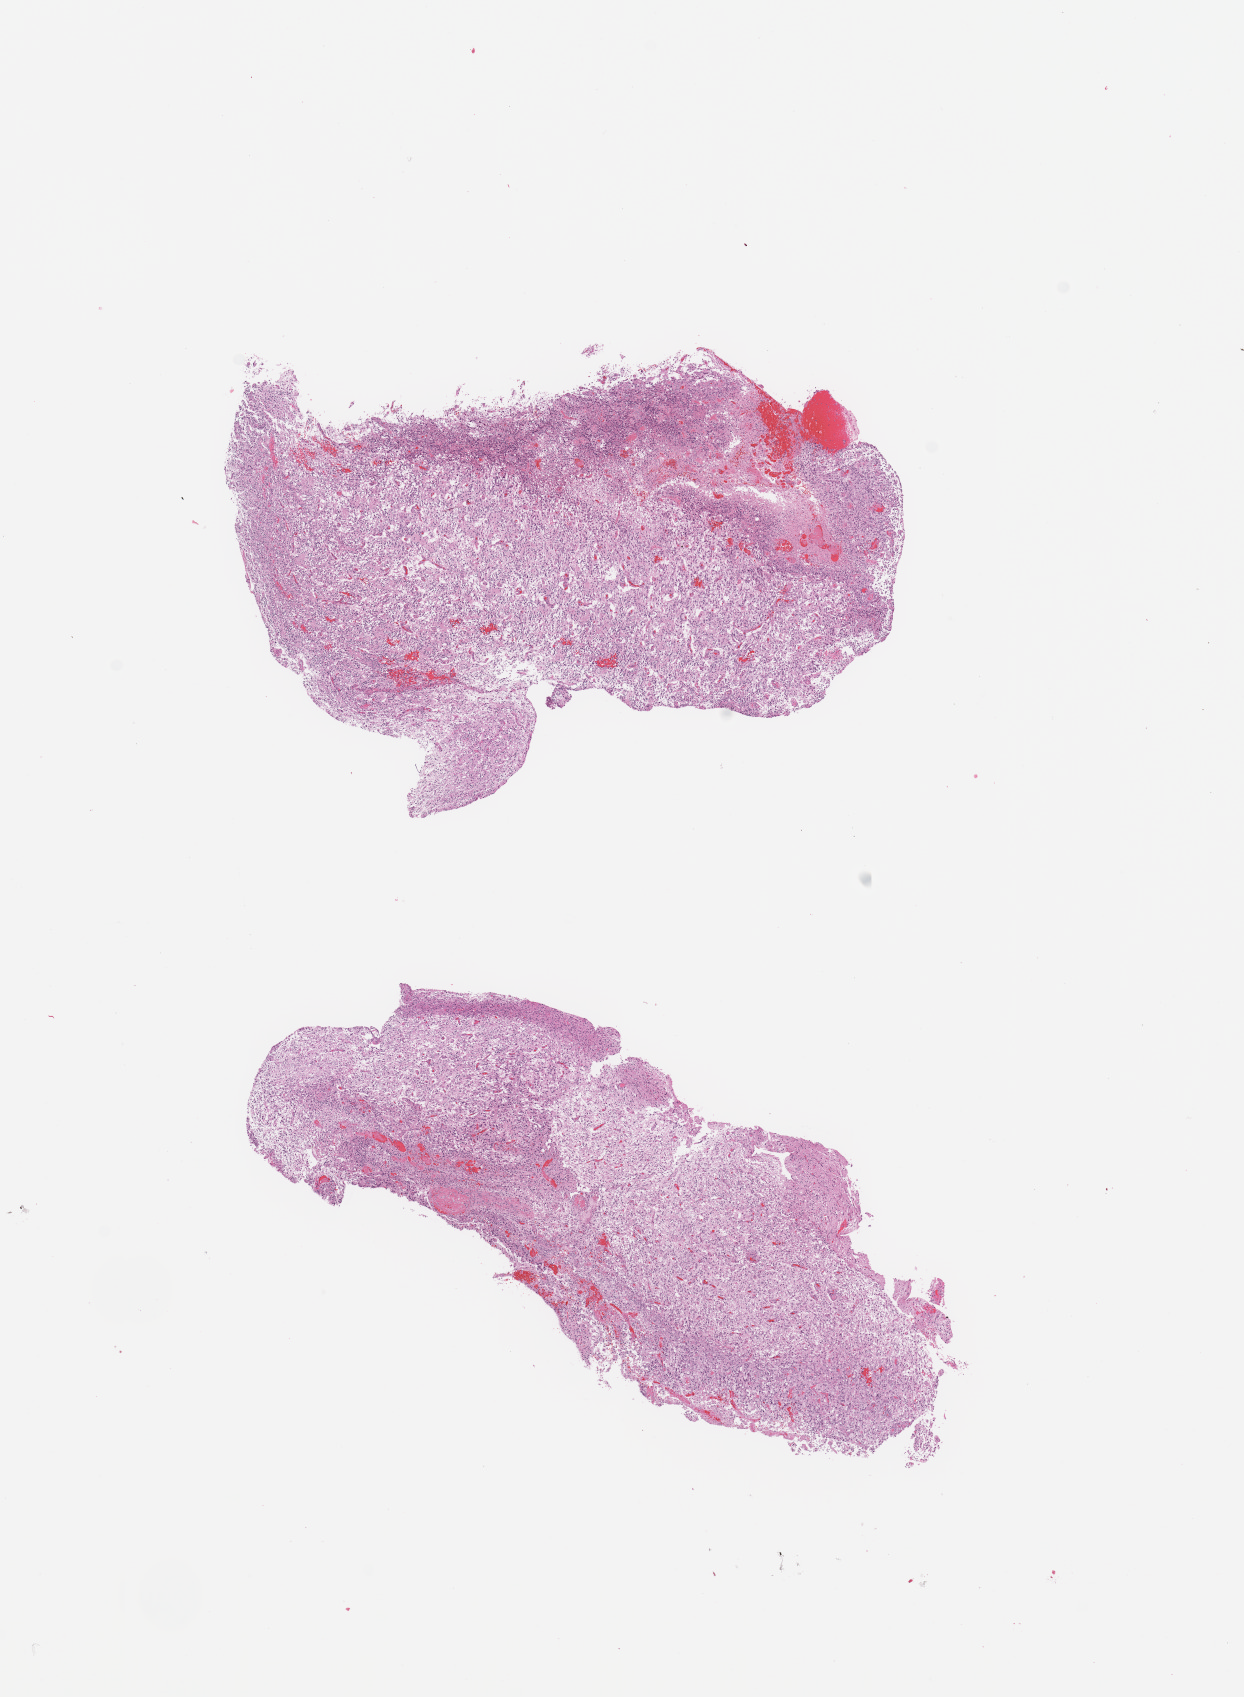
Whole-slide histology image, H&E-stained, a low-resolution overview of the entire scanned area, about 9.8 x 13.4 mm (acquisition: 20x scan), tumour tissue sample, sampled site: brain. 59-year-old male patient. Pathologist review of this section (percent, as recorded): tumour nuclei 75%, necrosis 10%.
* primary tumour site (as recorded): parietal lobe
* histologic diagnosis: Glioblastoma